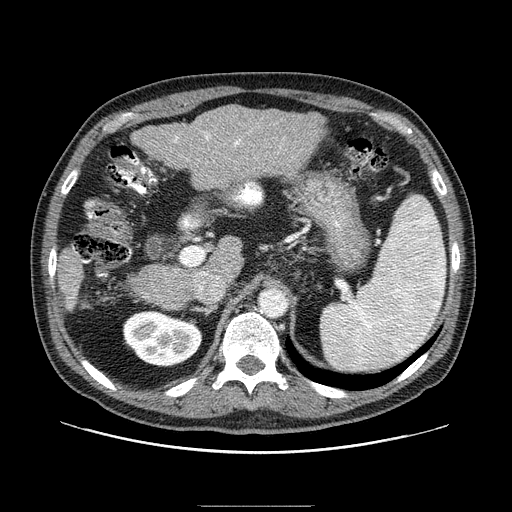
Contrast-enhanced abdominal CT (liver protocol), one axial slice; position 49 of 99 along the scan axis; reconstruction kernel STANDARD; 100 kVp; one of 2 acquisitions stored at this slice position; soft-tissue window (W 400 / L 40 HU); 2.5 mm slice thickness; 512 × 512 image matrix, field of view 400 × 400 mm. Case-level facts recorded for this patient, not image findings: diagnosis: hepatocellular carcinoma (patient treated with transarterial chemoembolisation; whether this scan precedes or follows treatment is not stated here); TNM stage (as recorded): Stage-II; Child-Pugh class: A; tumour differentiation: well differentiated; tumour nodularity: multinodular.
Structures marked on this image (semi-automatically segmented with operator editing):
- liver parenchyma outside the tumour (the mass and vessels are separate outlines, so this box may not span the whole liver): bounding box [x1, y1, x2, y2] px = [58, 106, 324, 310]
- liver vessels: [174, 134, 240, 146]